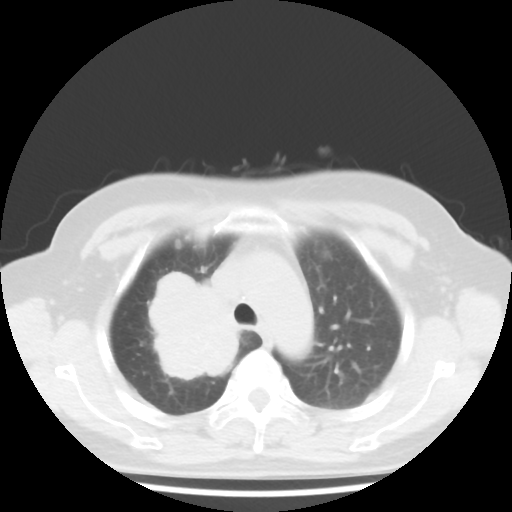
Chest CT, one axial slice. Reconstruction kernel STANDARD. Lung window (W 1500 / L -600 HU). 5 mm slice thickness. 512 × 512 image matrix. Patient: female, 62 years. From the clinical record (not read from this slice): clinical TNM (as recorded): T3 N0 M0.
Structures marked on this image (rectangle marked by the reading radiologist):
- lung tumour (recorded histology: small cell carcinoma): bounding box <146,259,245,395> (left, top, right, bottom; pixels)